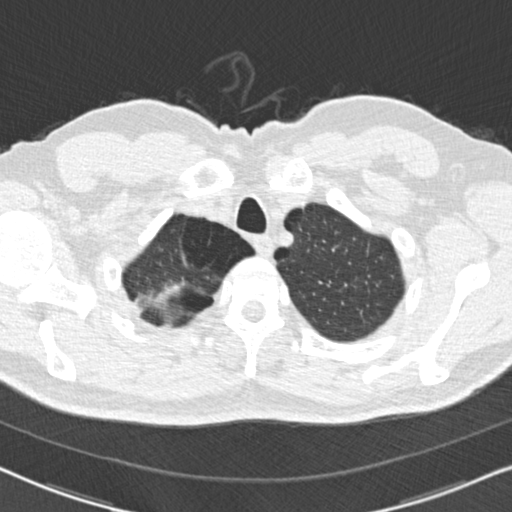
Chest CT (low-dose screening protocol), one axial image. Baseline annual screen. Lung window (W 1500 / L -600 HU). Standard (soft-tissue) reconstruction kernel (B30f). 120 kVp. Slice 20 of 152 in the series. Male participant, aged 56 years at enrolment.
- Expert reader's lesion annotation, box from (x=138, y=269) to (x=198, y=314) px.
- Screening reader's record for this exam: no non-calcified nodule ≥4 mm recorded.
- Official screen result: negative screen, minor abnormalities not suspicious for lung cancer.
- Participant outcome: lung cancer diagnosed 756 days after this screen — adenocarcinoma, NOS, right upper lobe, moderately differentiated (G2), stage IA (AJCC 6th edition), 9 mm at pathology.